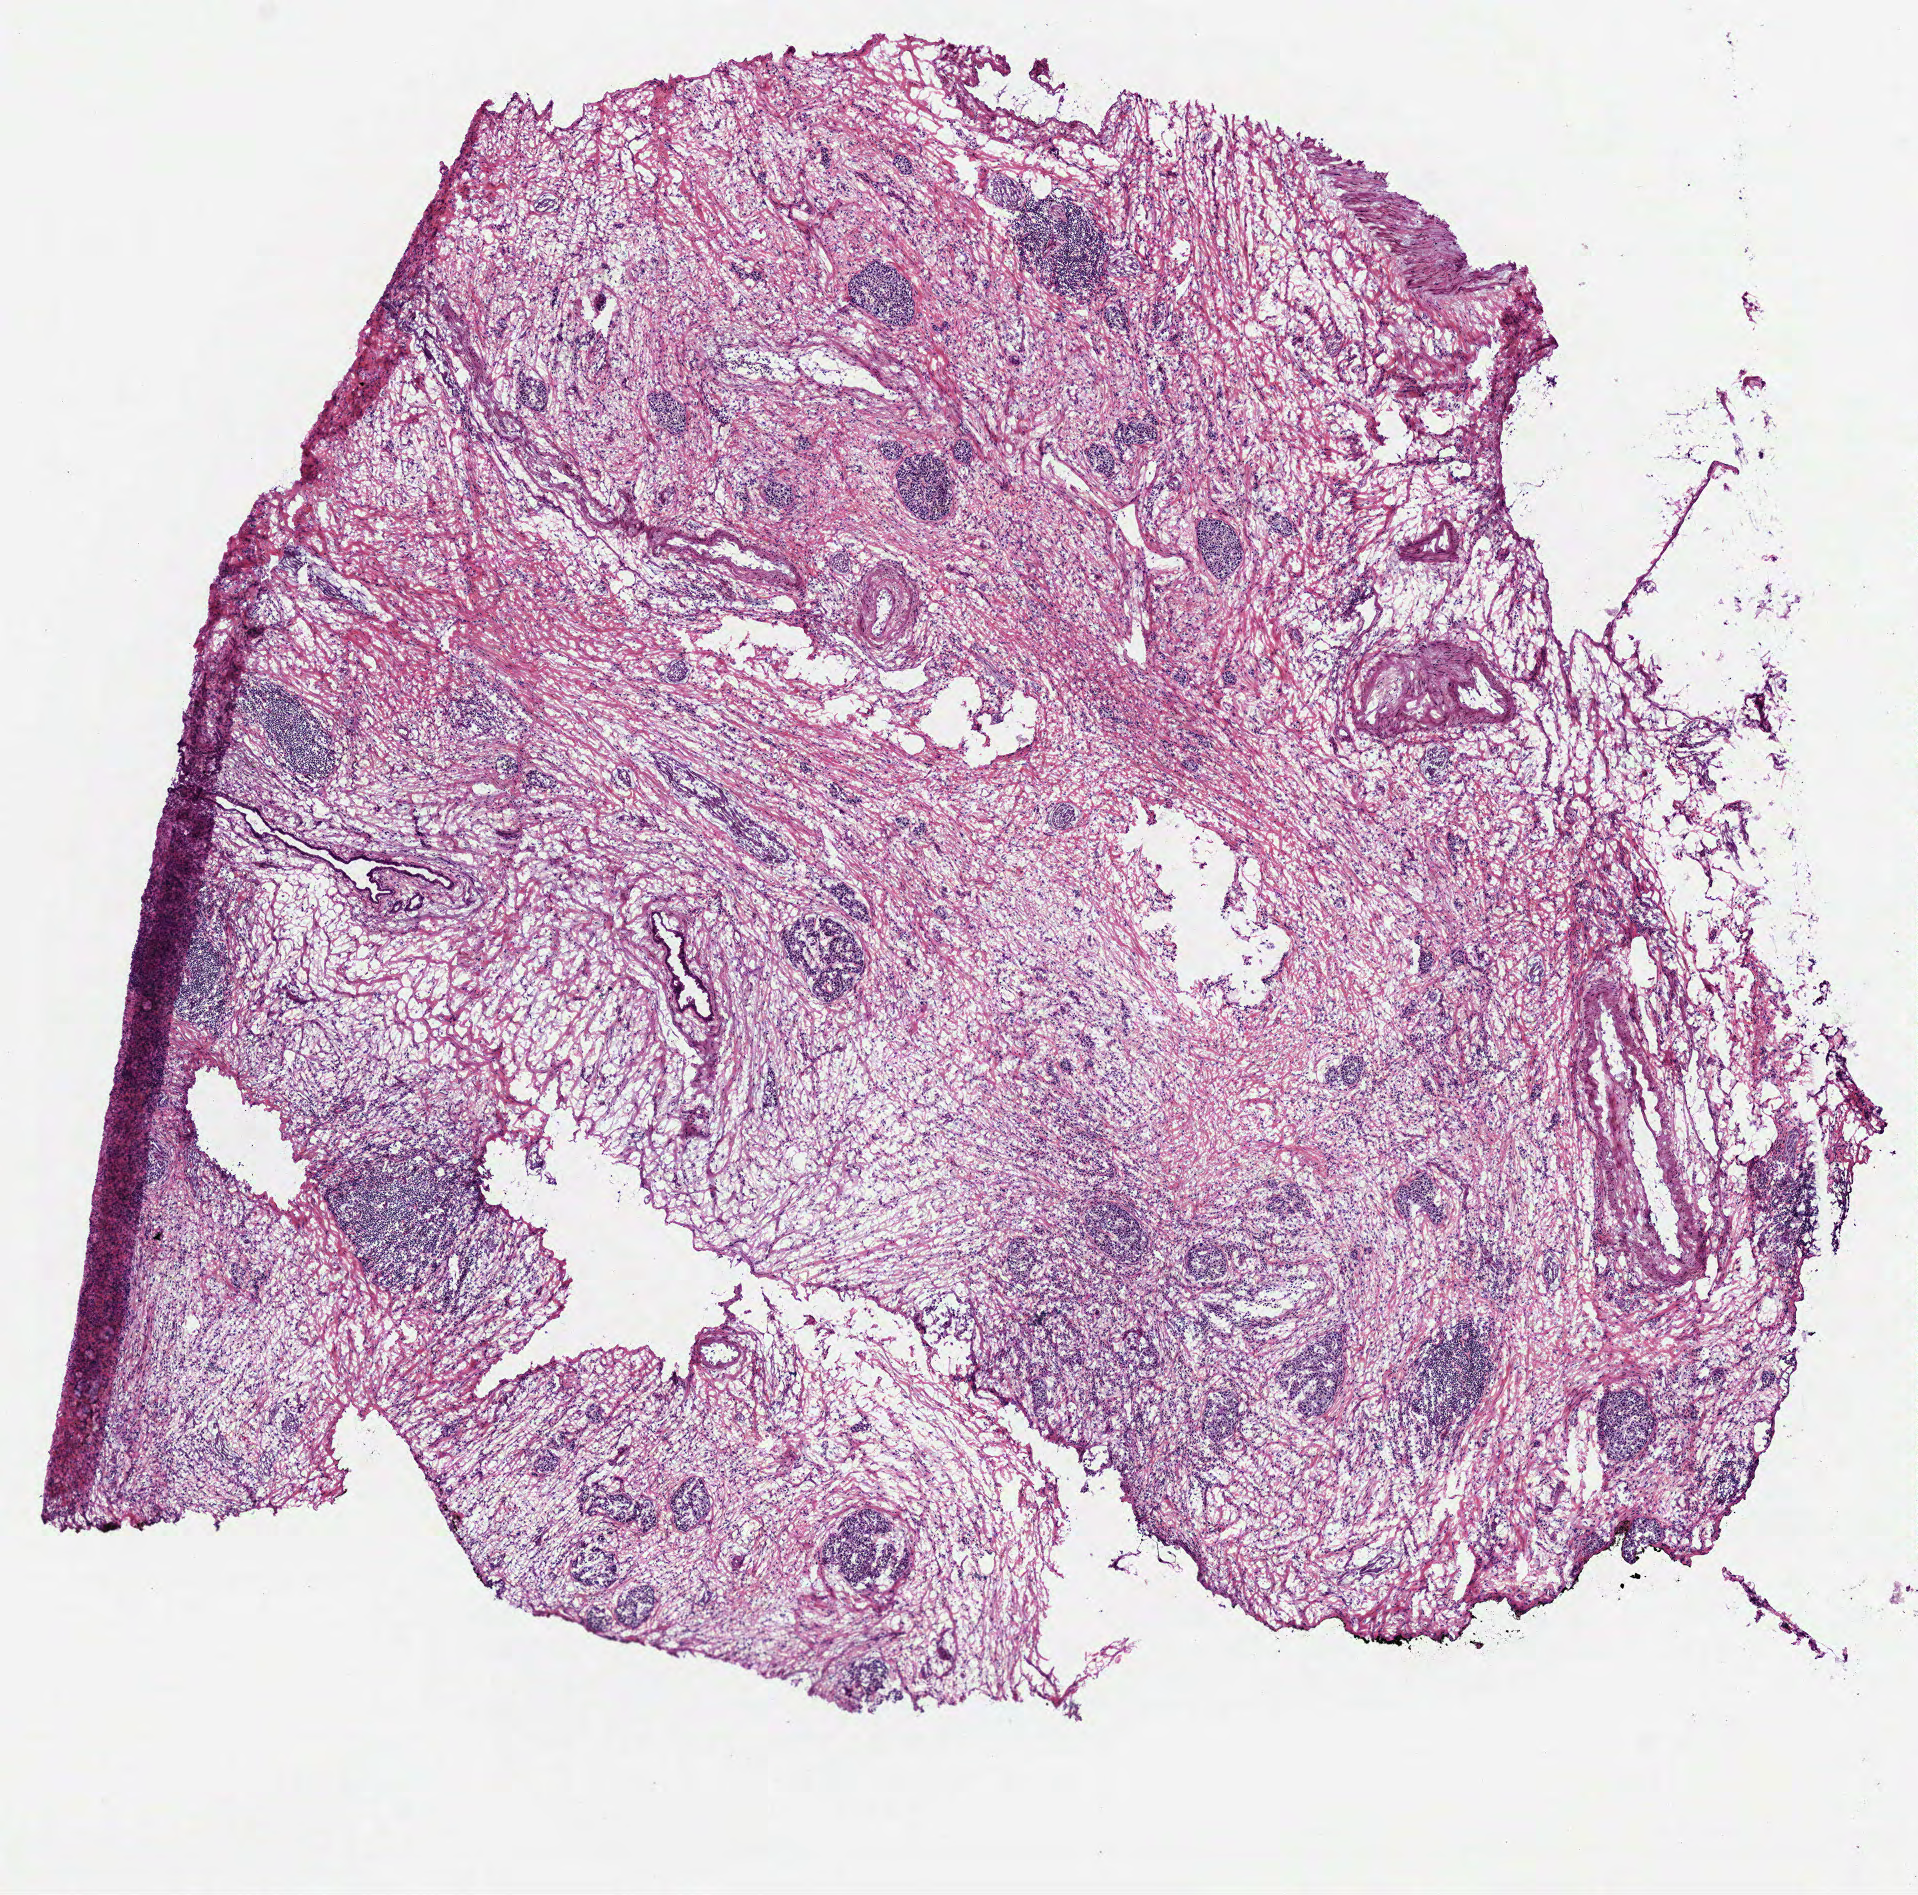
H&E-stained whole-slide image, shown as a low-resolution overview of the whole scanned area (about 7.7 x 7.6 mm). Frozen section from the bottom of the tissue portion. Sample: primary tumour, pancreas. Male, age 71 years at initial diagnosis. Histologic grade: G2 (moderately differentiated). Slide review estimates, as recorded: tumour cells 30%, tumour nuclei 50%, normal cells 0%, stromal cells 70%, necrosis 0%.
Lymph nodes positive (case pathology): 0 of 12 examined. TNM: T2 N0 MX. AJCC pathologic stage: IB (7th edition). Histologic diagnosis: Infiltrating duct carcinoma, NOS.